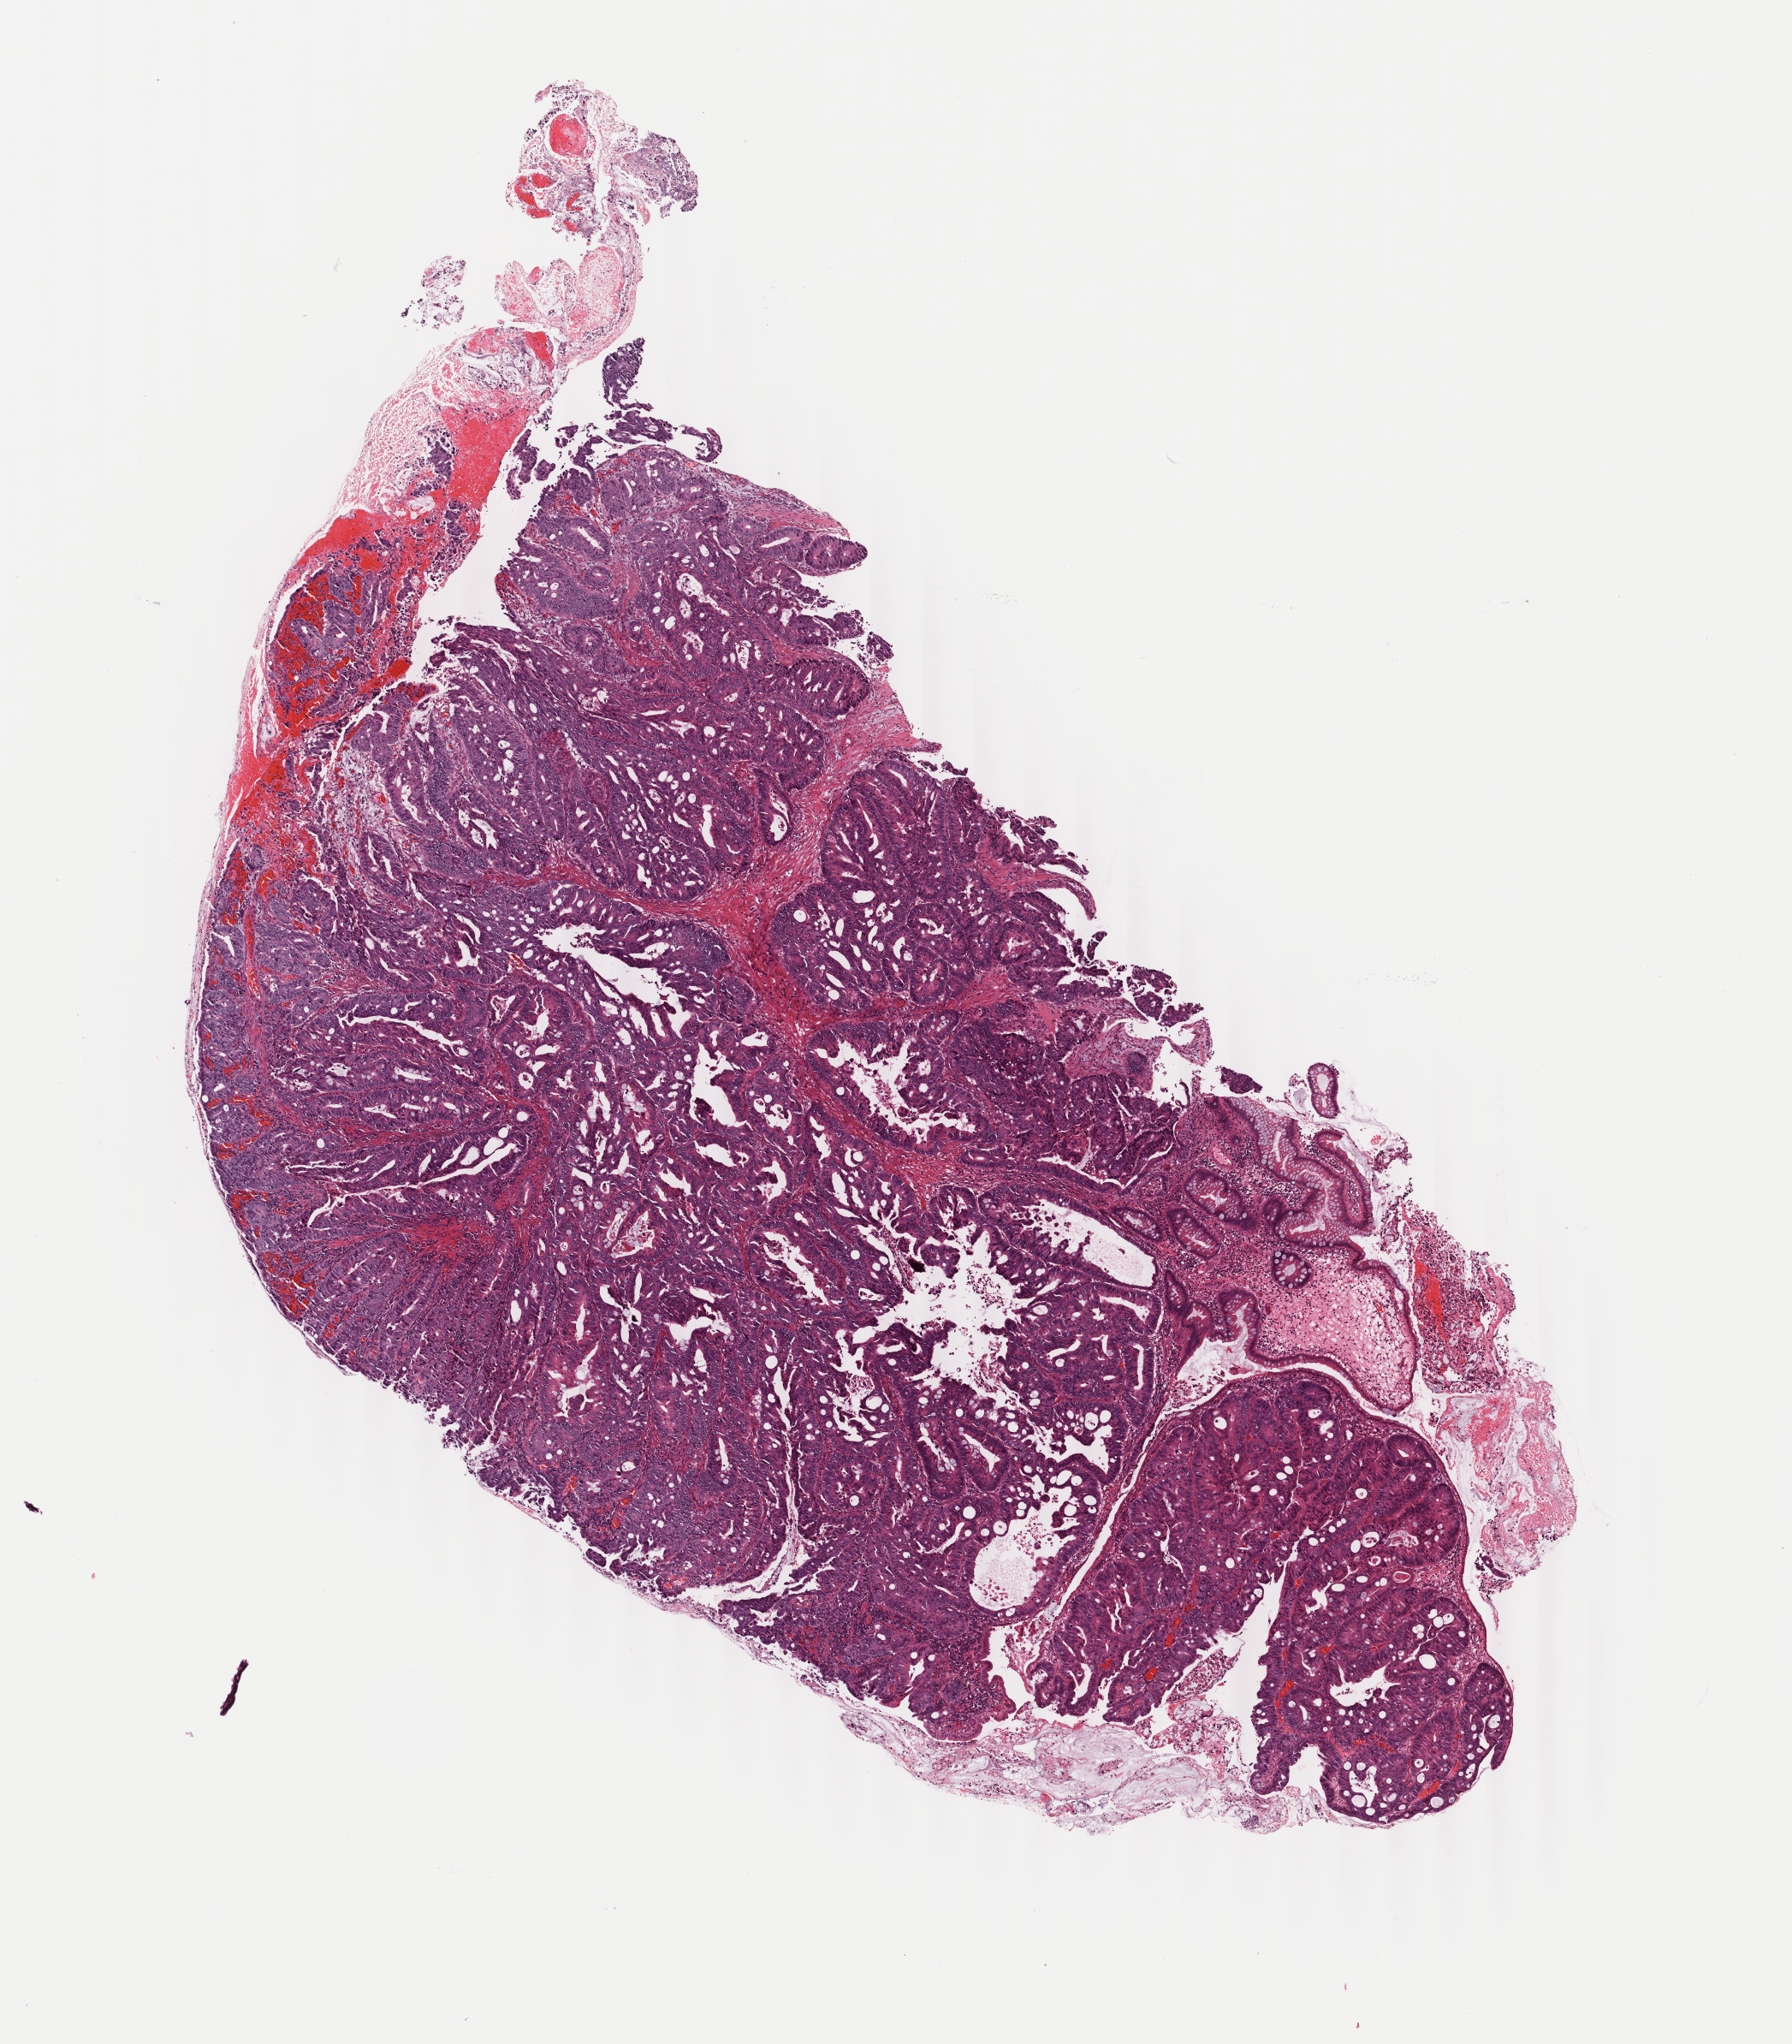
Hematoxylin and eosin (H&E) stained whole-slide image — shown as a low-resolution overview of the whole scanned area (about 8.3 x 9.5 mm, slide scanned at 40x). Frozen section from the bottom of the tissue portion. Primary tumour sample from the colon. Female, age 69 years at initial diagnosis. Slide review estimates, as recorded: tumour cells 96%, tumour nuclei 92%, normal cells 4%, stromal cells 0%, necrosis 0%. Infiltration values recorded for this section: lymphocyte infiltration 0%, monocyte infiltration 0%, neutrophil infiltration 0%.
Pathologic diagnosis: Adenocarcinoma, NOS (ascending colon). AJCC pathologic stage: IIA (7th edition).